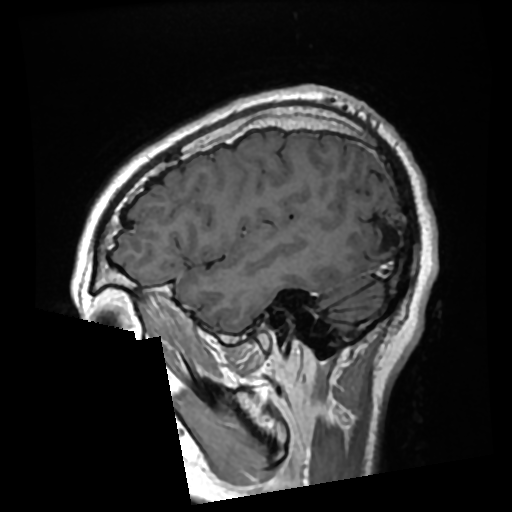
Brain MRI from a brain-tumour surgery series, one sagittal slice; slice 75 of 276 in the series (ordered by position); T1-weighted post-contrast; 0.7 mm slice thickness; 512 × 512 image matrix. From the clinical record (not read from this slice): histopathology: Glioma with ependymal features; WHO grade: 2.
Outlined on this slice (outlined manually by an expert reader):
- previous resection cavity: box from (x=366, y=220) to (x=395, y=251) px